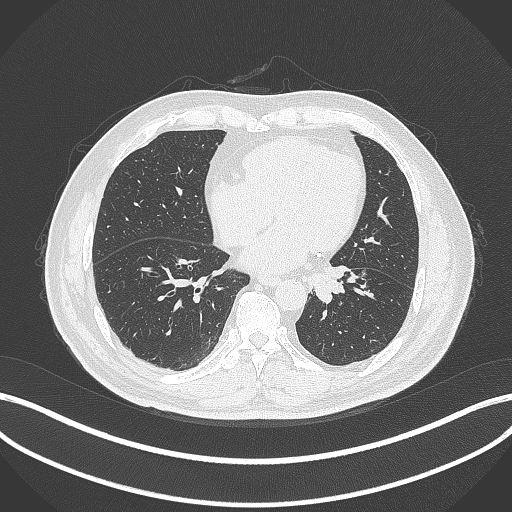
Chest CT, one axial slice; slice 97 of 312 in the series (ordered by position); 120 kVp; lung window (W 1500 / L -600 HU); 1 mm slice thickness; 512 × 512 image matrix, field of view 400 × 400 mm. Patient: male, 71 years. Case-level facts recorded for this patient, not image findings: clinical TNM (as recorded): T1b N0 M0.
Outlined on this slice (rectangle marked by the reading radiologist):
- lung tumour (recorded histology: squamous cell carcinoma): bounding box [x1, y1, x2, y2] px = [306, 264, 357, 303]